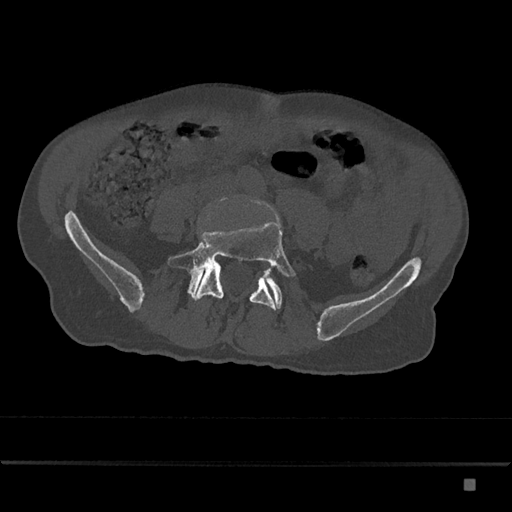
CT including the spine, one axial slice. Position 279 of 797 along the scan axis. Reconstruction kernel Br40s/3. Bone window (W 1800 / L 400 HU). 0.5 mm slice thickness. 512 × 512 image matrix, field of view 390 × 390 mm. Male patient, age 72 years. From the clinical record (not read from this slice): primary cancer: prostate.
Outlined on this slice (semi-automatically segmented with operator editing):
- L5 vertebra: bounding box [x1, y1, x2, y2] px = [167, 203, 295, 310]